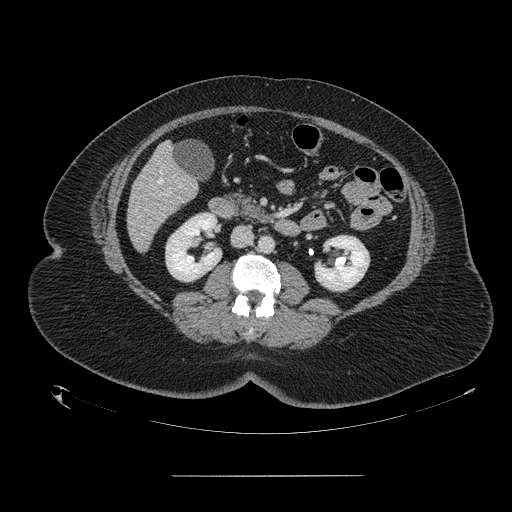
Contrast-enhanced abdominal CT, one axial slice. Position 51 of 164 along the scan axis. 120 kVp. Intravenous contrast given. Soft-tissue window (W 400 / L 40 HU). 512 × 512 image matrix. Female patient, age 52 years. Case-level facts recorded for this patient, not image findings: diagnosis: colorectal cancer liver metastases, imaged before liver resection; multiple liver metastases: yes; largest metastasis: 3.5 cm; disease in both lobes: no.
Outlined on this slice (expert manual segmentation):
- hepatic veins: bounding box [x1, y1, x2, y2] px = [158, 170, 162, 184]
- liver: [128, 145, 198, 251]
- portal vein (with intrahepatic branches): [161, 193, 168, 196]